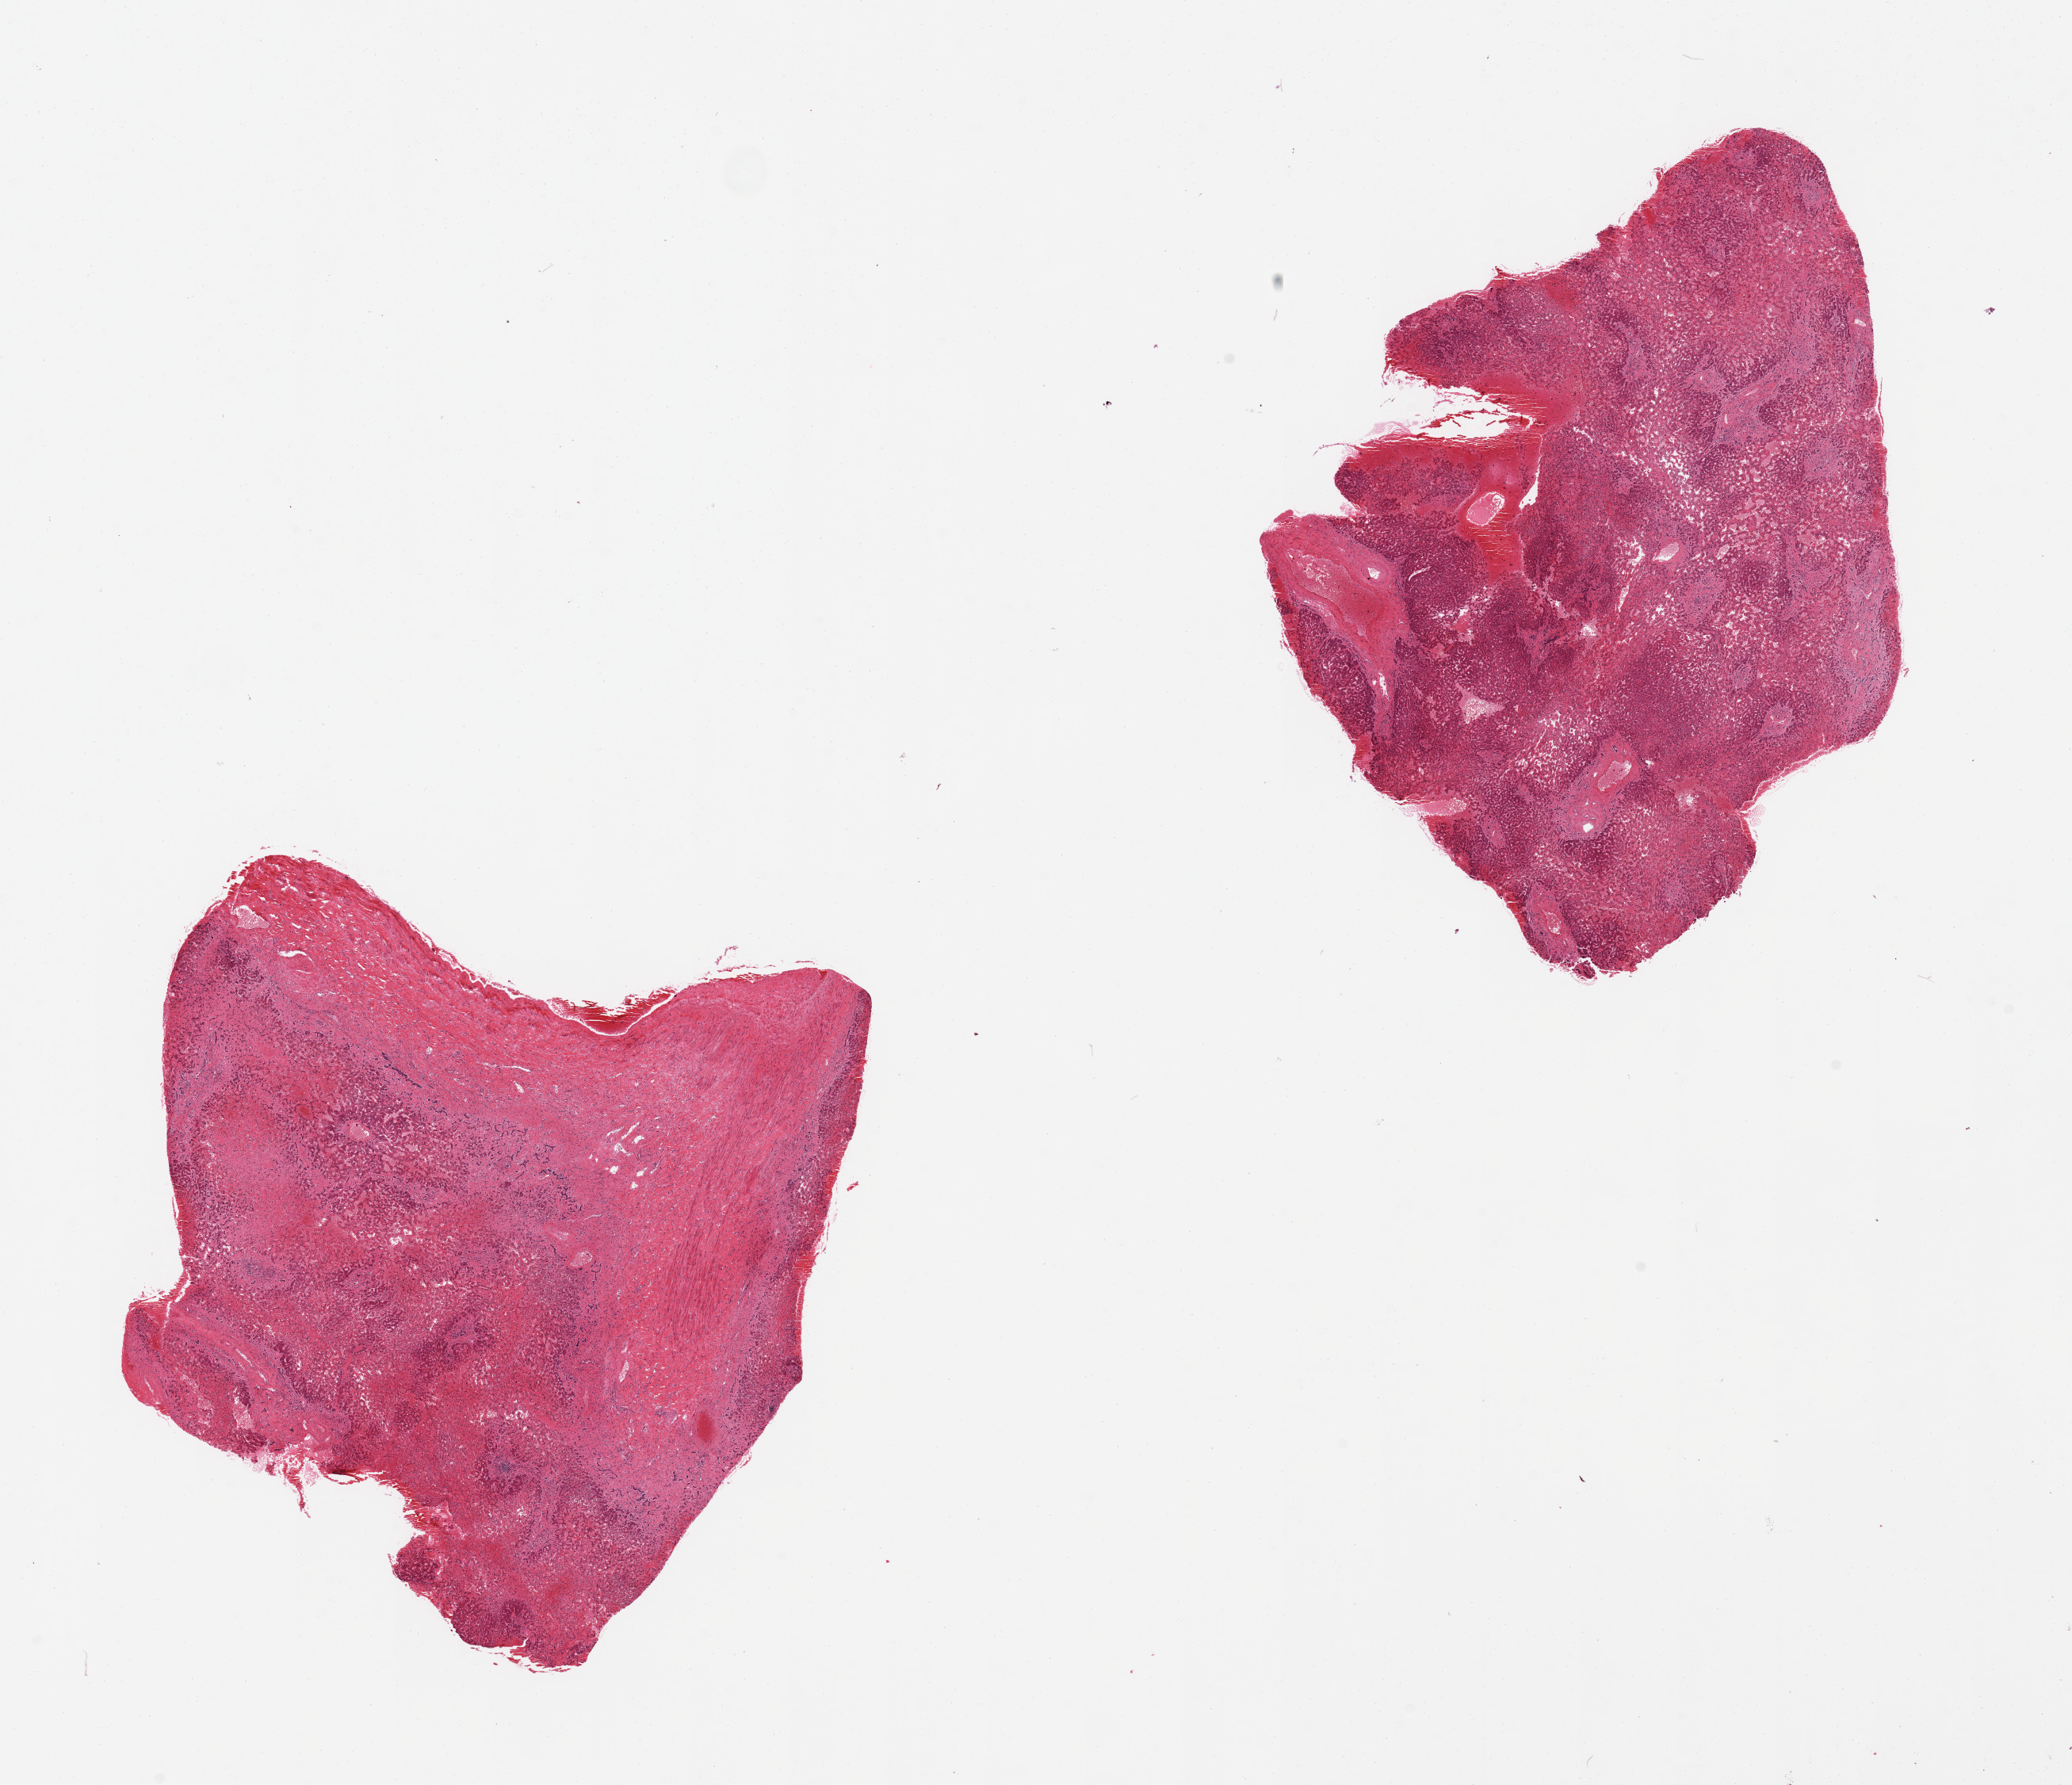
Digitized hematoxylin and eosin (H&E)-stained section, low-resolution overview of the scanned area, about 20.7 x 17.8 mm (from a 20x scan), PAXgene-fixed, paraffin-embedded tissue, section of liver (target tissue), tissue donor sample. Donor sex: female.
Reviewer comment on this tissue sample: 2 pieces, subtotal massive hepatic necrosis.